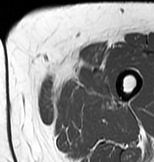
MRI of an extremity soft-tissue mass, one axial slice; position 11 of 83 along the scan axis; MR volume resampled by the dataset authors to the PET/CT grid (not the native acquisition matrix); 3.27 mm slice thickness; 154 × 162 image matrix. Female patient. Case-level facts recorded for this patient, not image findings: histological type: myxofibrosarcoma; grade: intermediate; site of the primary tumour: left thigh.
Annotated regions visible in this slice (expert contour drawn on MRI and transferred to this co-registered scan by the dataset authors):
- gross tumour volume including surrounding oedema: bounding box [x1, y1, x2, y2] px = [40, 64, 113, 106]